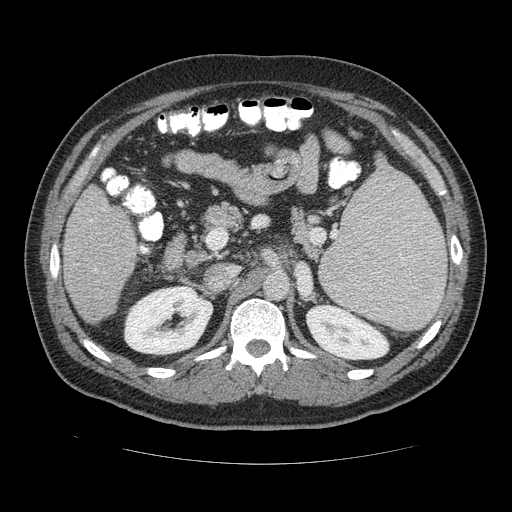
Contrast-enhanced abdominal CT (liver protocol), one axial slice. Position 64 of 113 along the scan axis. 120 kVp. Soft-tissue window (W 400 / L 40 HU). 2.5 mm slice thickness. 512 × 512 image matrix, field of view 400 × 400 mm. Case-level facts recorded for this patient, not image findings: diagnosis: hepatocellular carcinoma (patient treated with transarterial chemoembolisation; whether this scan precedes or follows treatment is not stated here); TNM stage (as recorded): Stage-II; Child-Pugh class: B; tumour nodularity: multinodular.
Annotated regions visible in this slice (semi-automatic segmentation, software-assisted and operator-edited):
- liver parenchyma outside the tumour (the mass and vessels are separate outlines, so this box may not span the whole liver): bounding box <62,182,140,326> (left, top, right, bottom; pixels)
- liver vessels: <89,208,102,272>